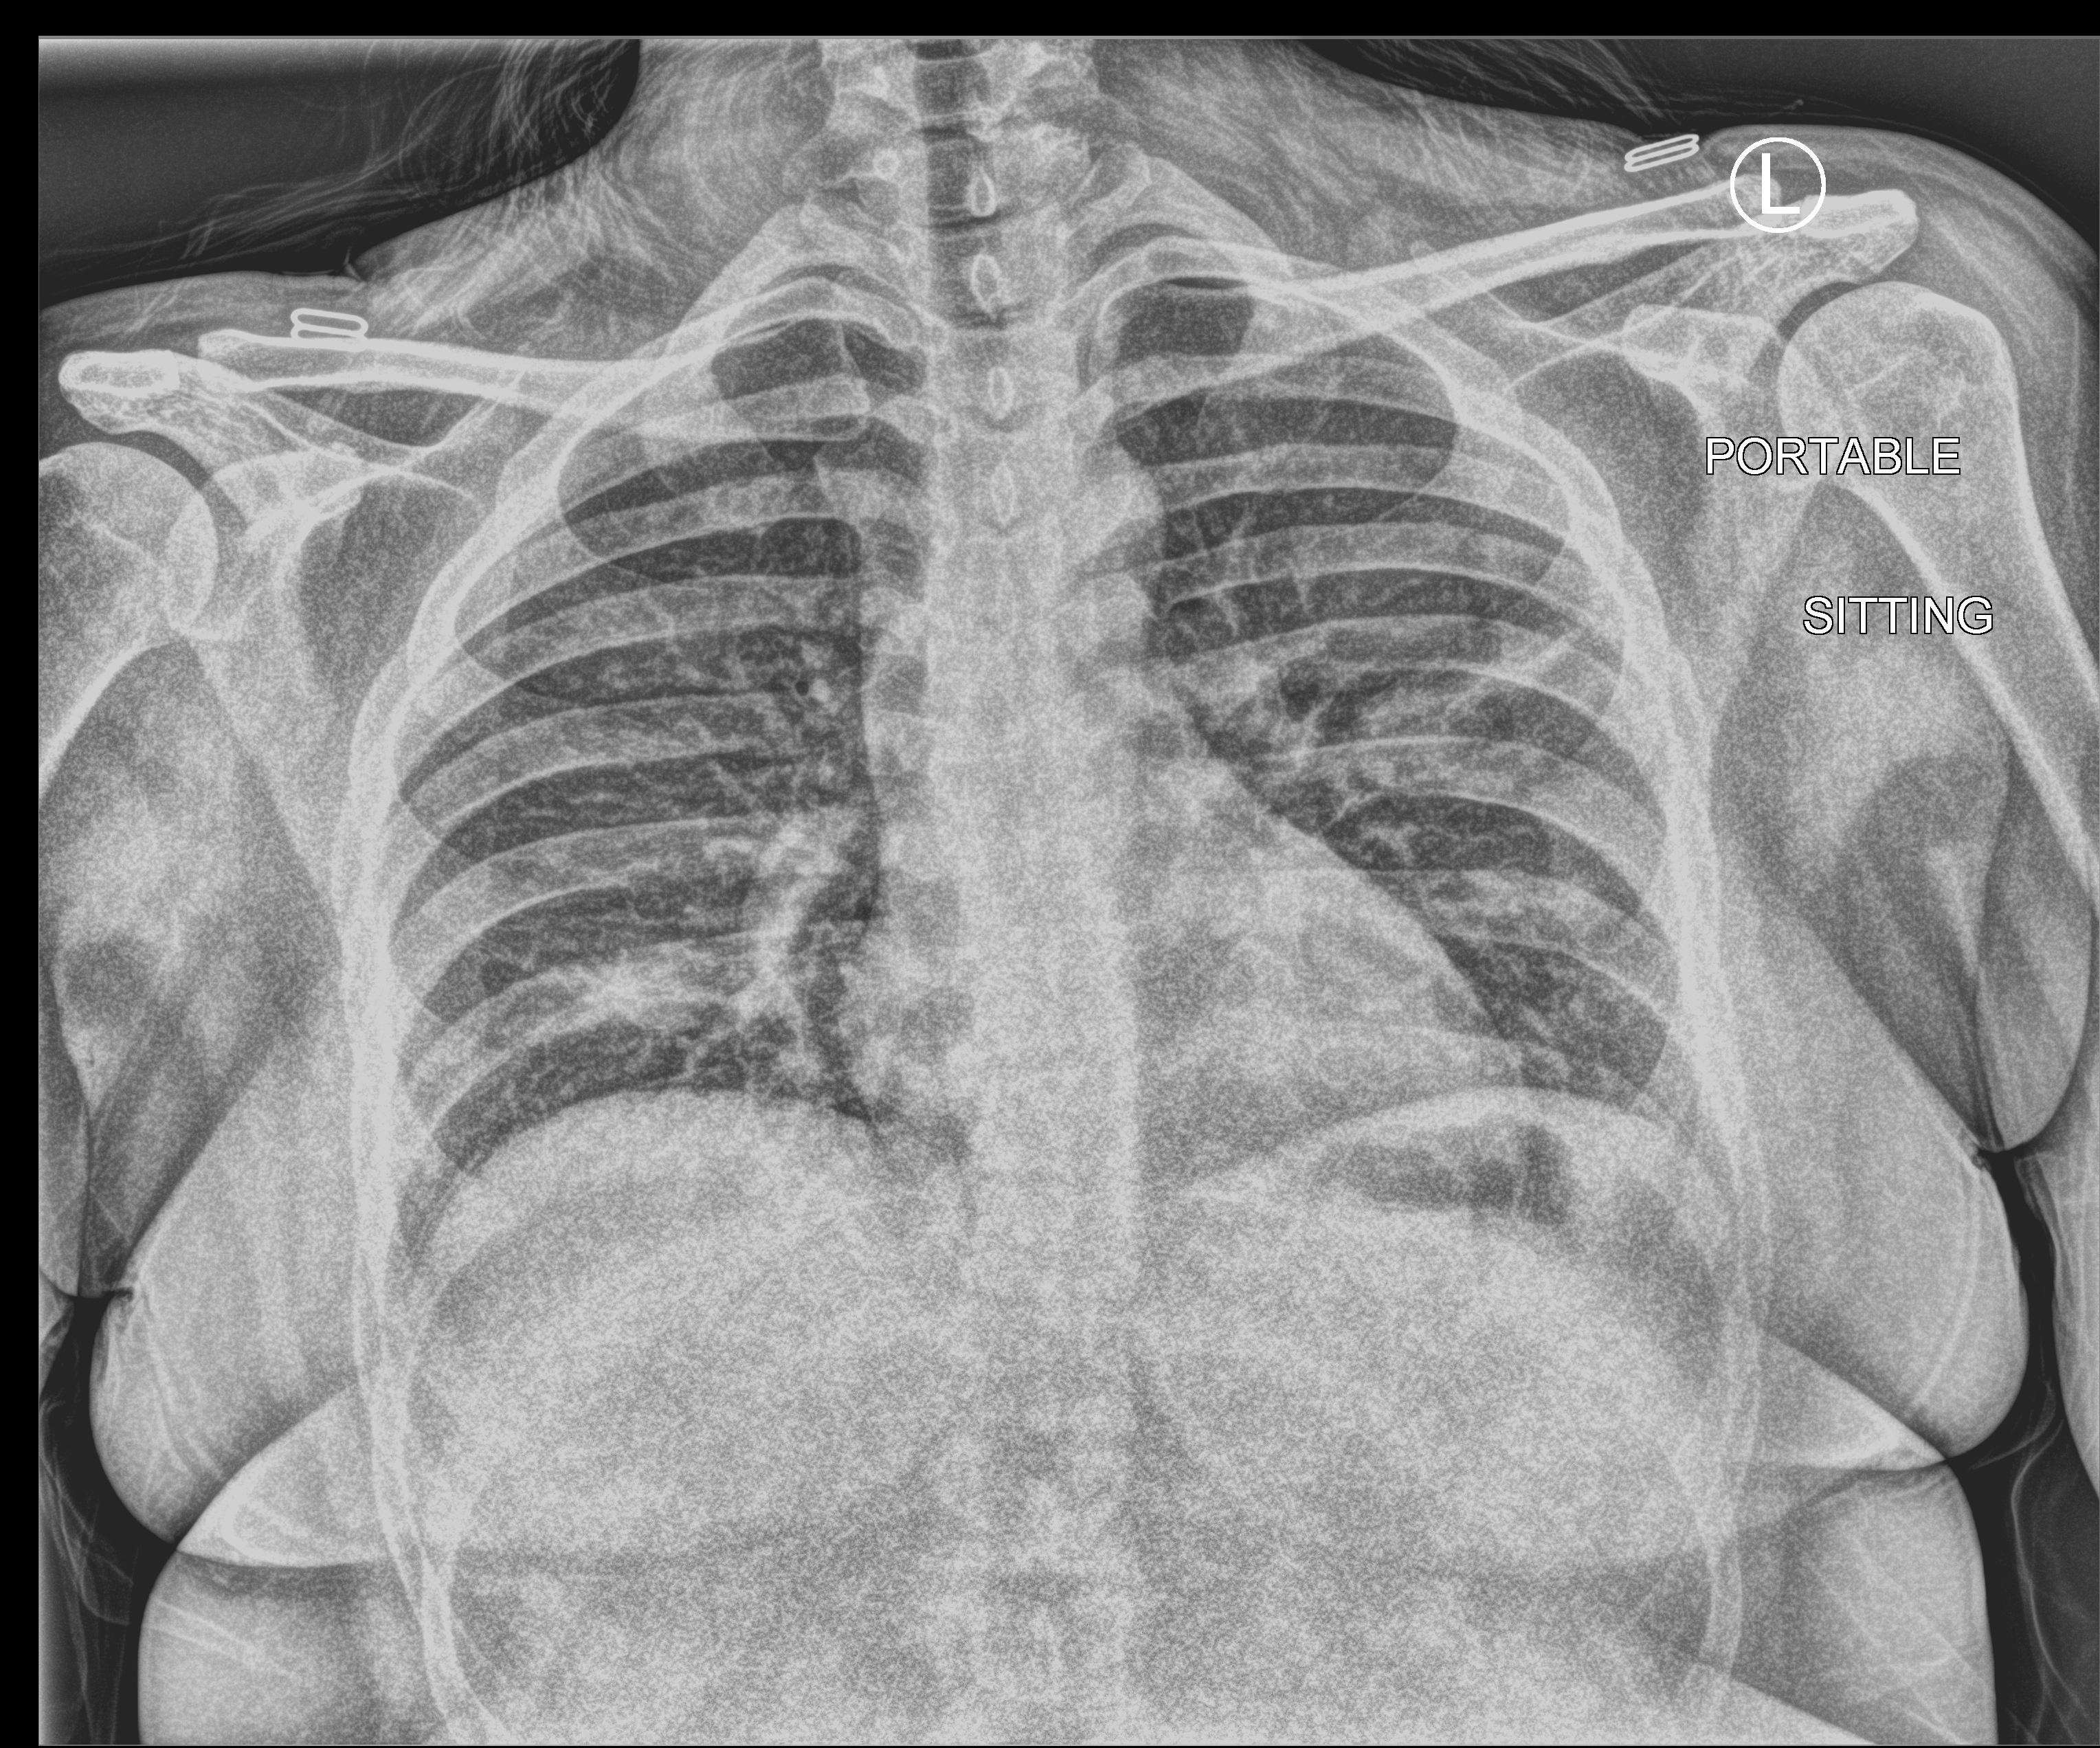
Bedside chest radiograph (computed radiography); anteroposterior (AP) projection. Female patient hospitalised with COVID-19, age 18–59 years.
Admission-level facts for this patient (not findings on this image; timing relative to this image not recorded):
- smoking status (admission record): never